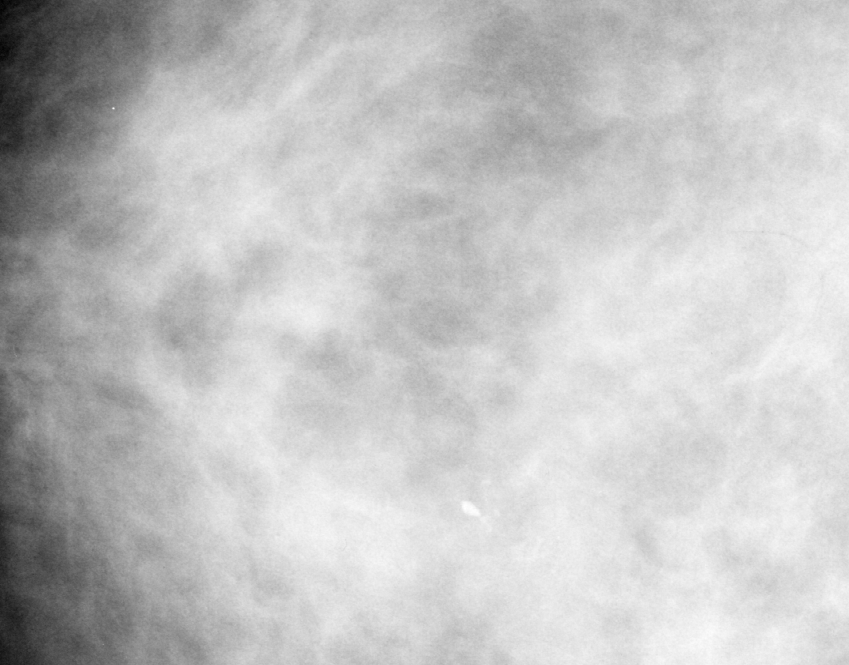
Region of interest cut from a scanned film mammogram (one marked finding), right breast, CC view, BI-RADS breast density category 2 (scale 1–4).
Finding: calcifications, morphology punctate, distribution clustered; BI-RADS assessment category 3; pathology result (as recorded, not read from the image): malignant.